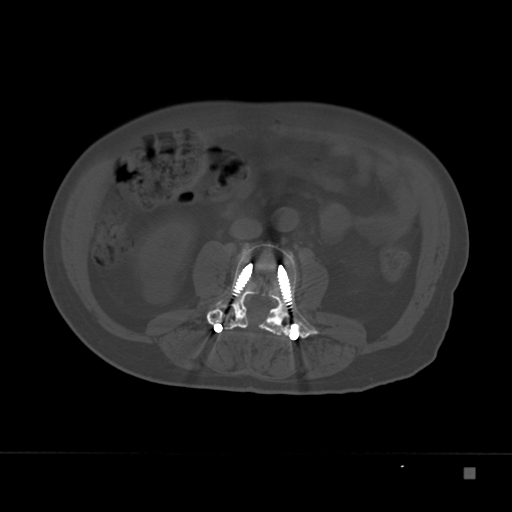
CT including the spine, one axial slice. Position 68 of 332 along the scan axis. Reconstruction kernel Br40s. 120 kVp. Bone window (W 1800 / L 400 HU). 1.5 mm slice thickness. 512 × 512 image matrix, field of view 389 × 389 mm. Patient: male, 72 years. Case-level facts recorded for this patient, not image findings: primary cancer: skeletal.
Annotated regions visible in this slice (semi-automatically segmented with operator editing):
- L3 vertebra: bounding box [x1, y1, x2, y2] px = [207, 243, 320, 340]